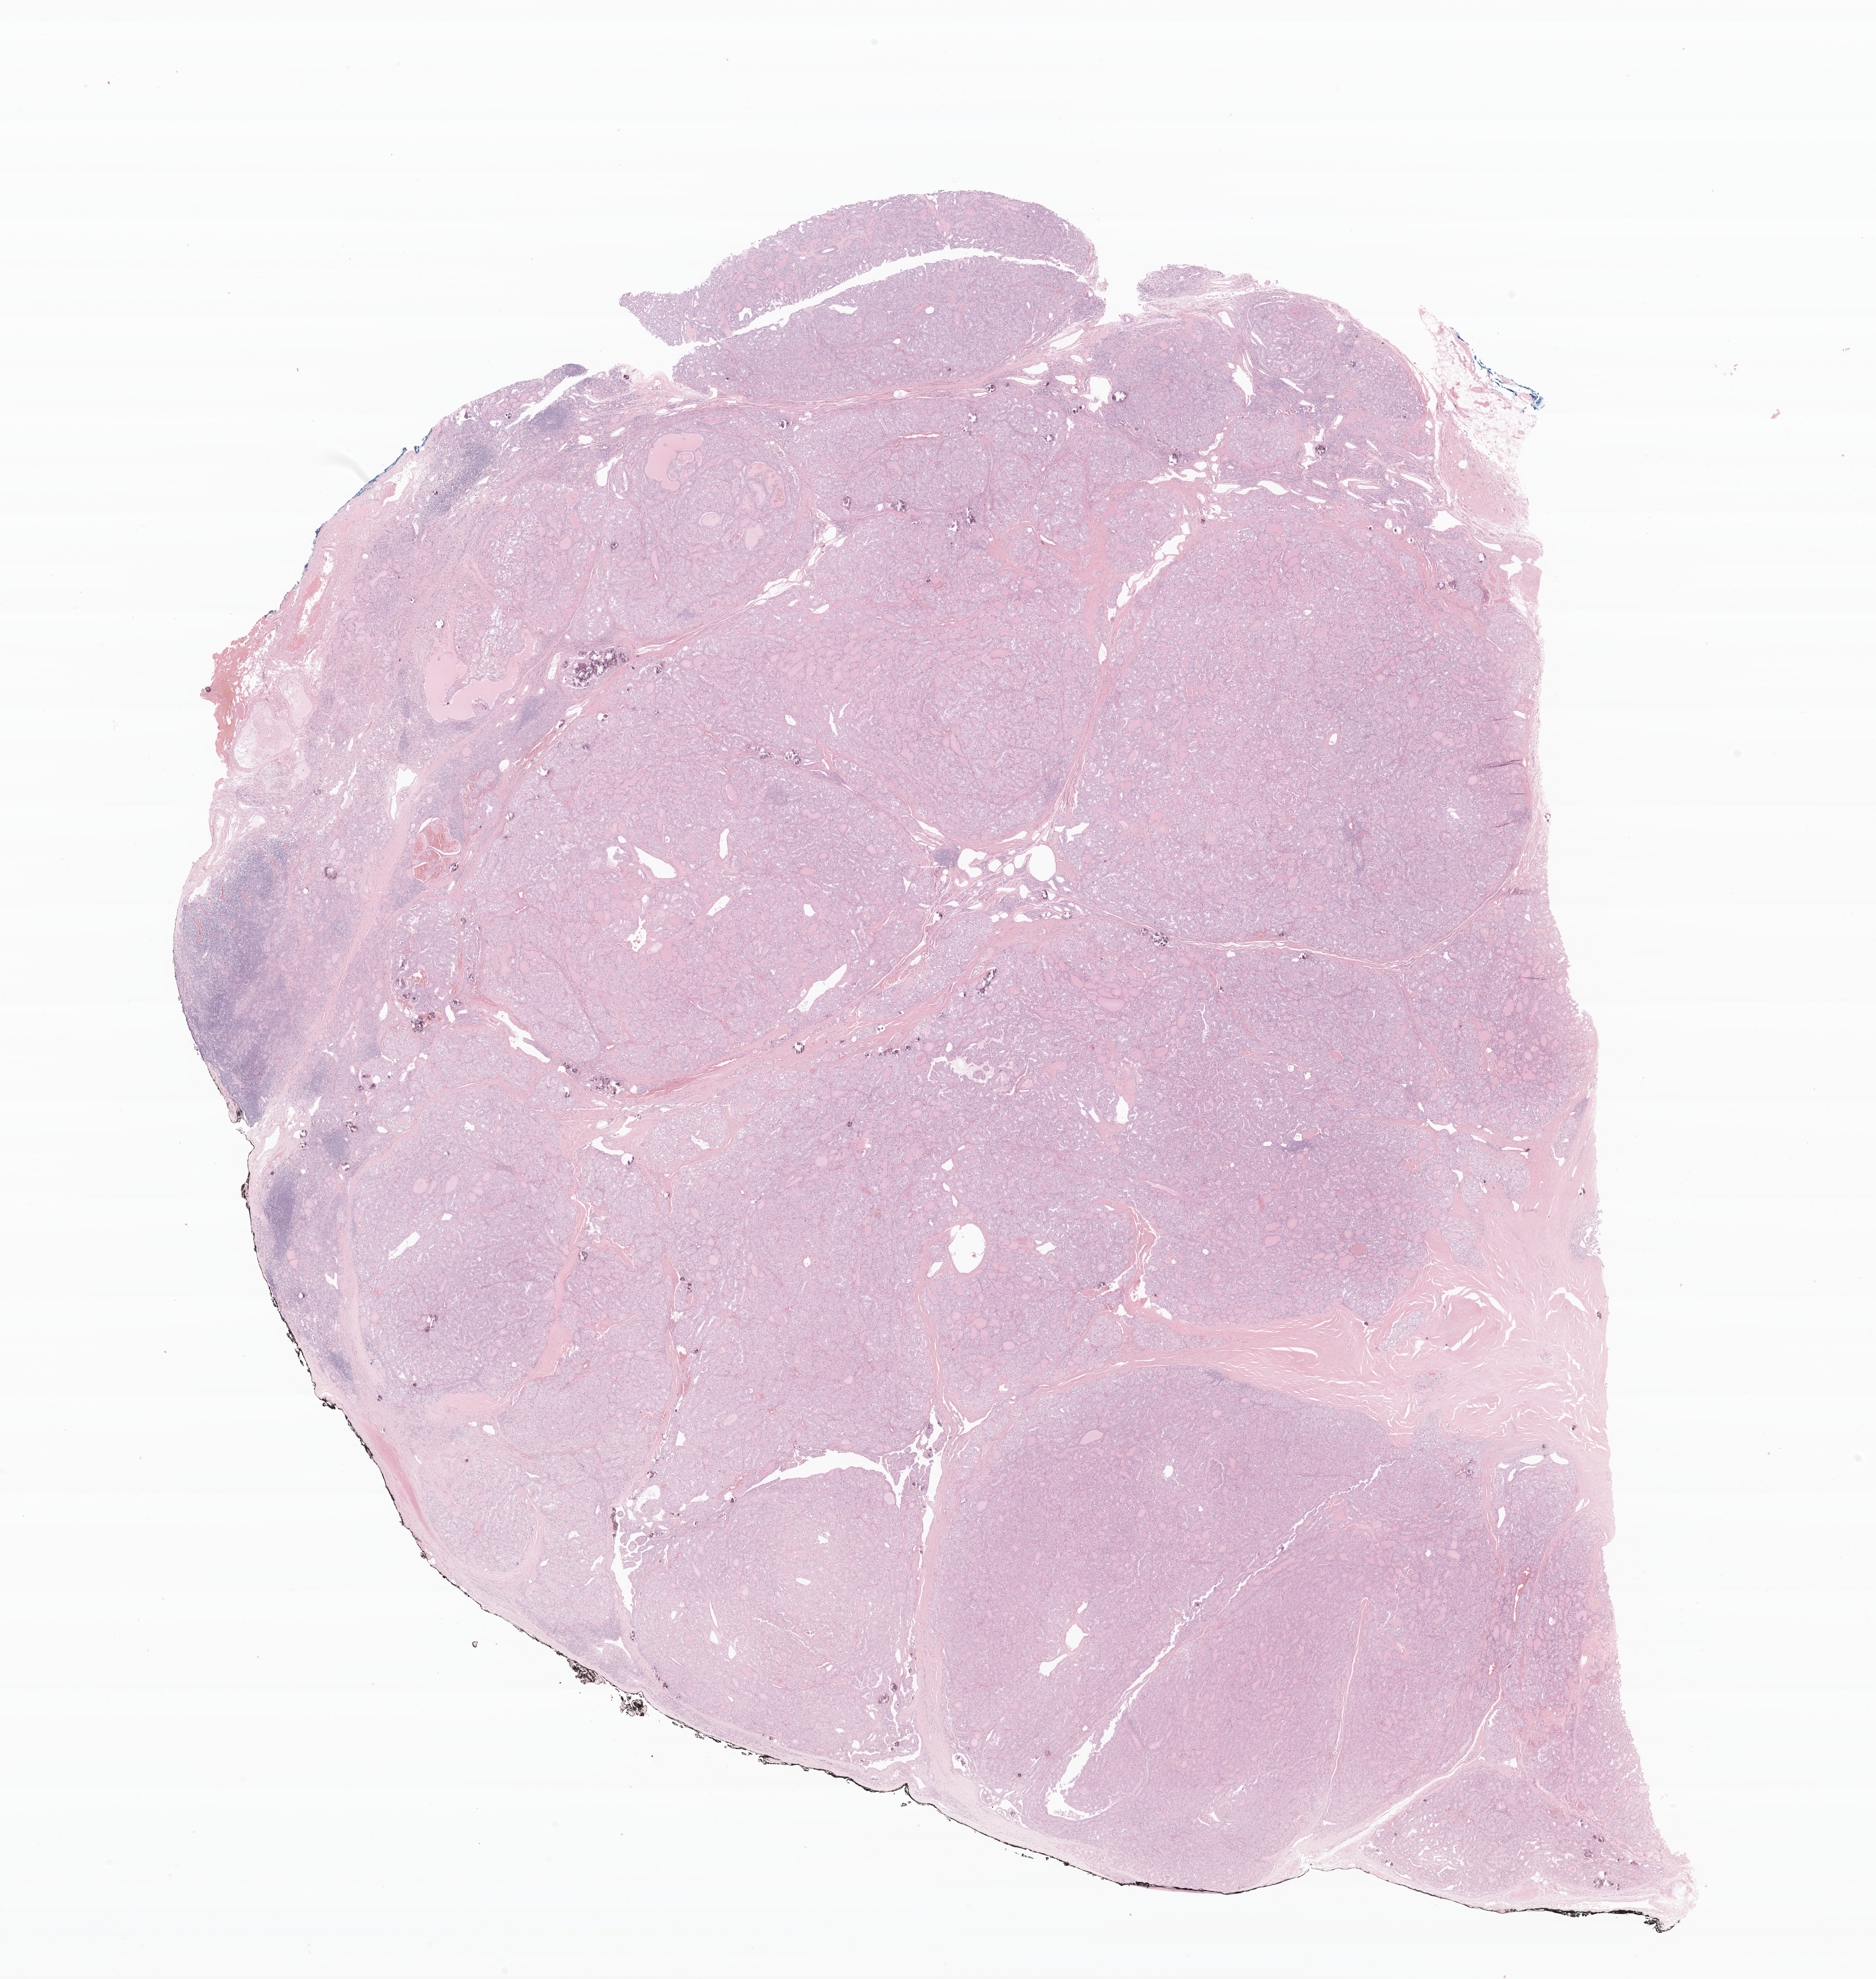
Whole-slide image, hematoxylin and eosin (H&E) stain of tumor tissue from the thyroid, low-resolution overview of the scanned area, about 20.4 x 21.5 mm. Formalin-fixed, paraffin-embedded (FFPE) tissue. Patient: male, age 219 months (18 years 3 months).
- recorded diagnosis: Papillary carcinoma, NOS